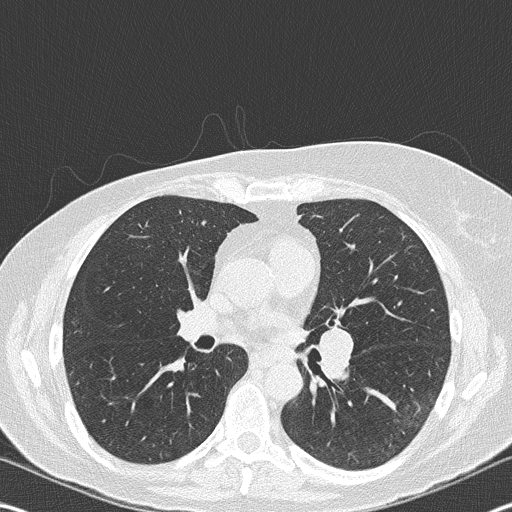
Low-dose screening chest CT, one axial slice. Reconstruction kernel B50f. 120 kVp. Lung window (W 1500 / L -600 HU). 2 mm slice thickness. 512 × 512 image matrix, field of view 342 × 342 mm.
Outlined on this slice (manually delineated by an expert):
- lesion 2 (nodule, hilum of left lung): bounding box <321,329,352,375> (left, top, right, bottom; pixels)